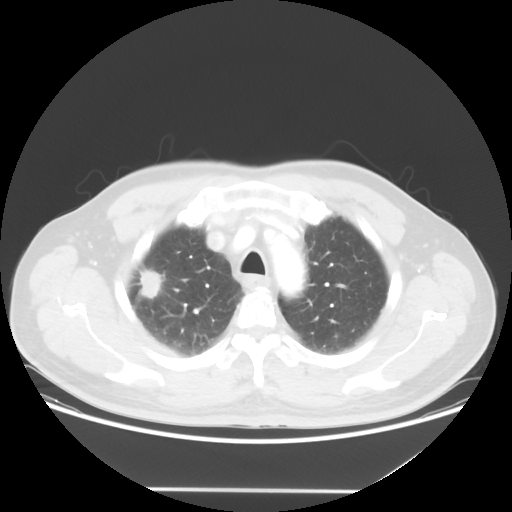
Chest CT, one axial slice. Position 43 of 54 along the scan axis. Reconstruction kernel STANDARD. Lung window (W 1500 / L -600 HU). 5 mm slice thickness. 512 × 512 image matrix, field of view 416 × 416 mm. Patient: male, 65 years. From the clinical record (not read from this slice): clinical TNM (as recorded): T1c N1 M0.
Structures marked on this image (rectangle marked by the reading radiologist):
- lung tumour (recorded histology: adenocarcinoma): bounding box (x1, y1, x2, y2) in pixels: (128, 260, 169, 315)